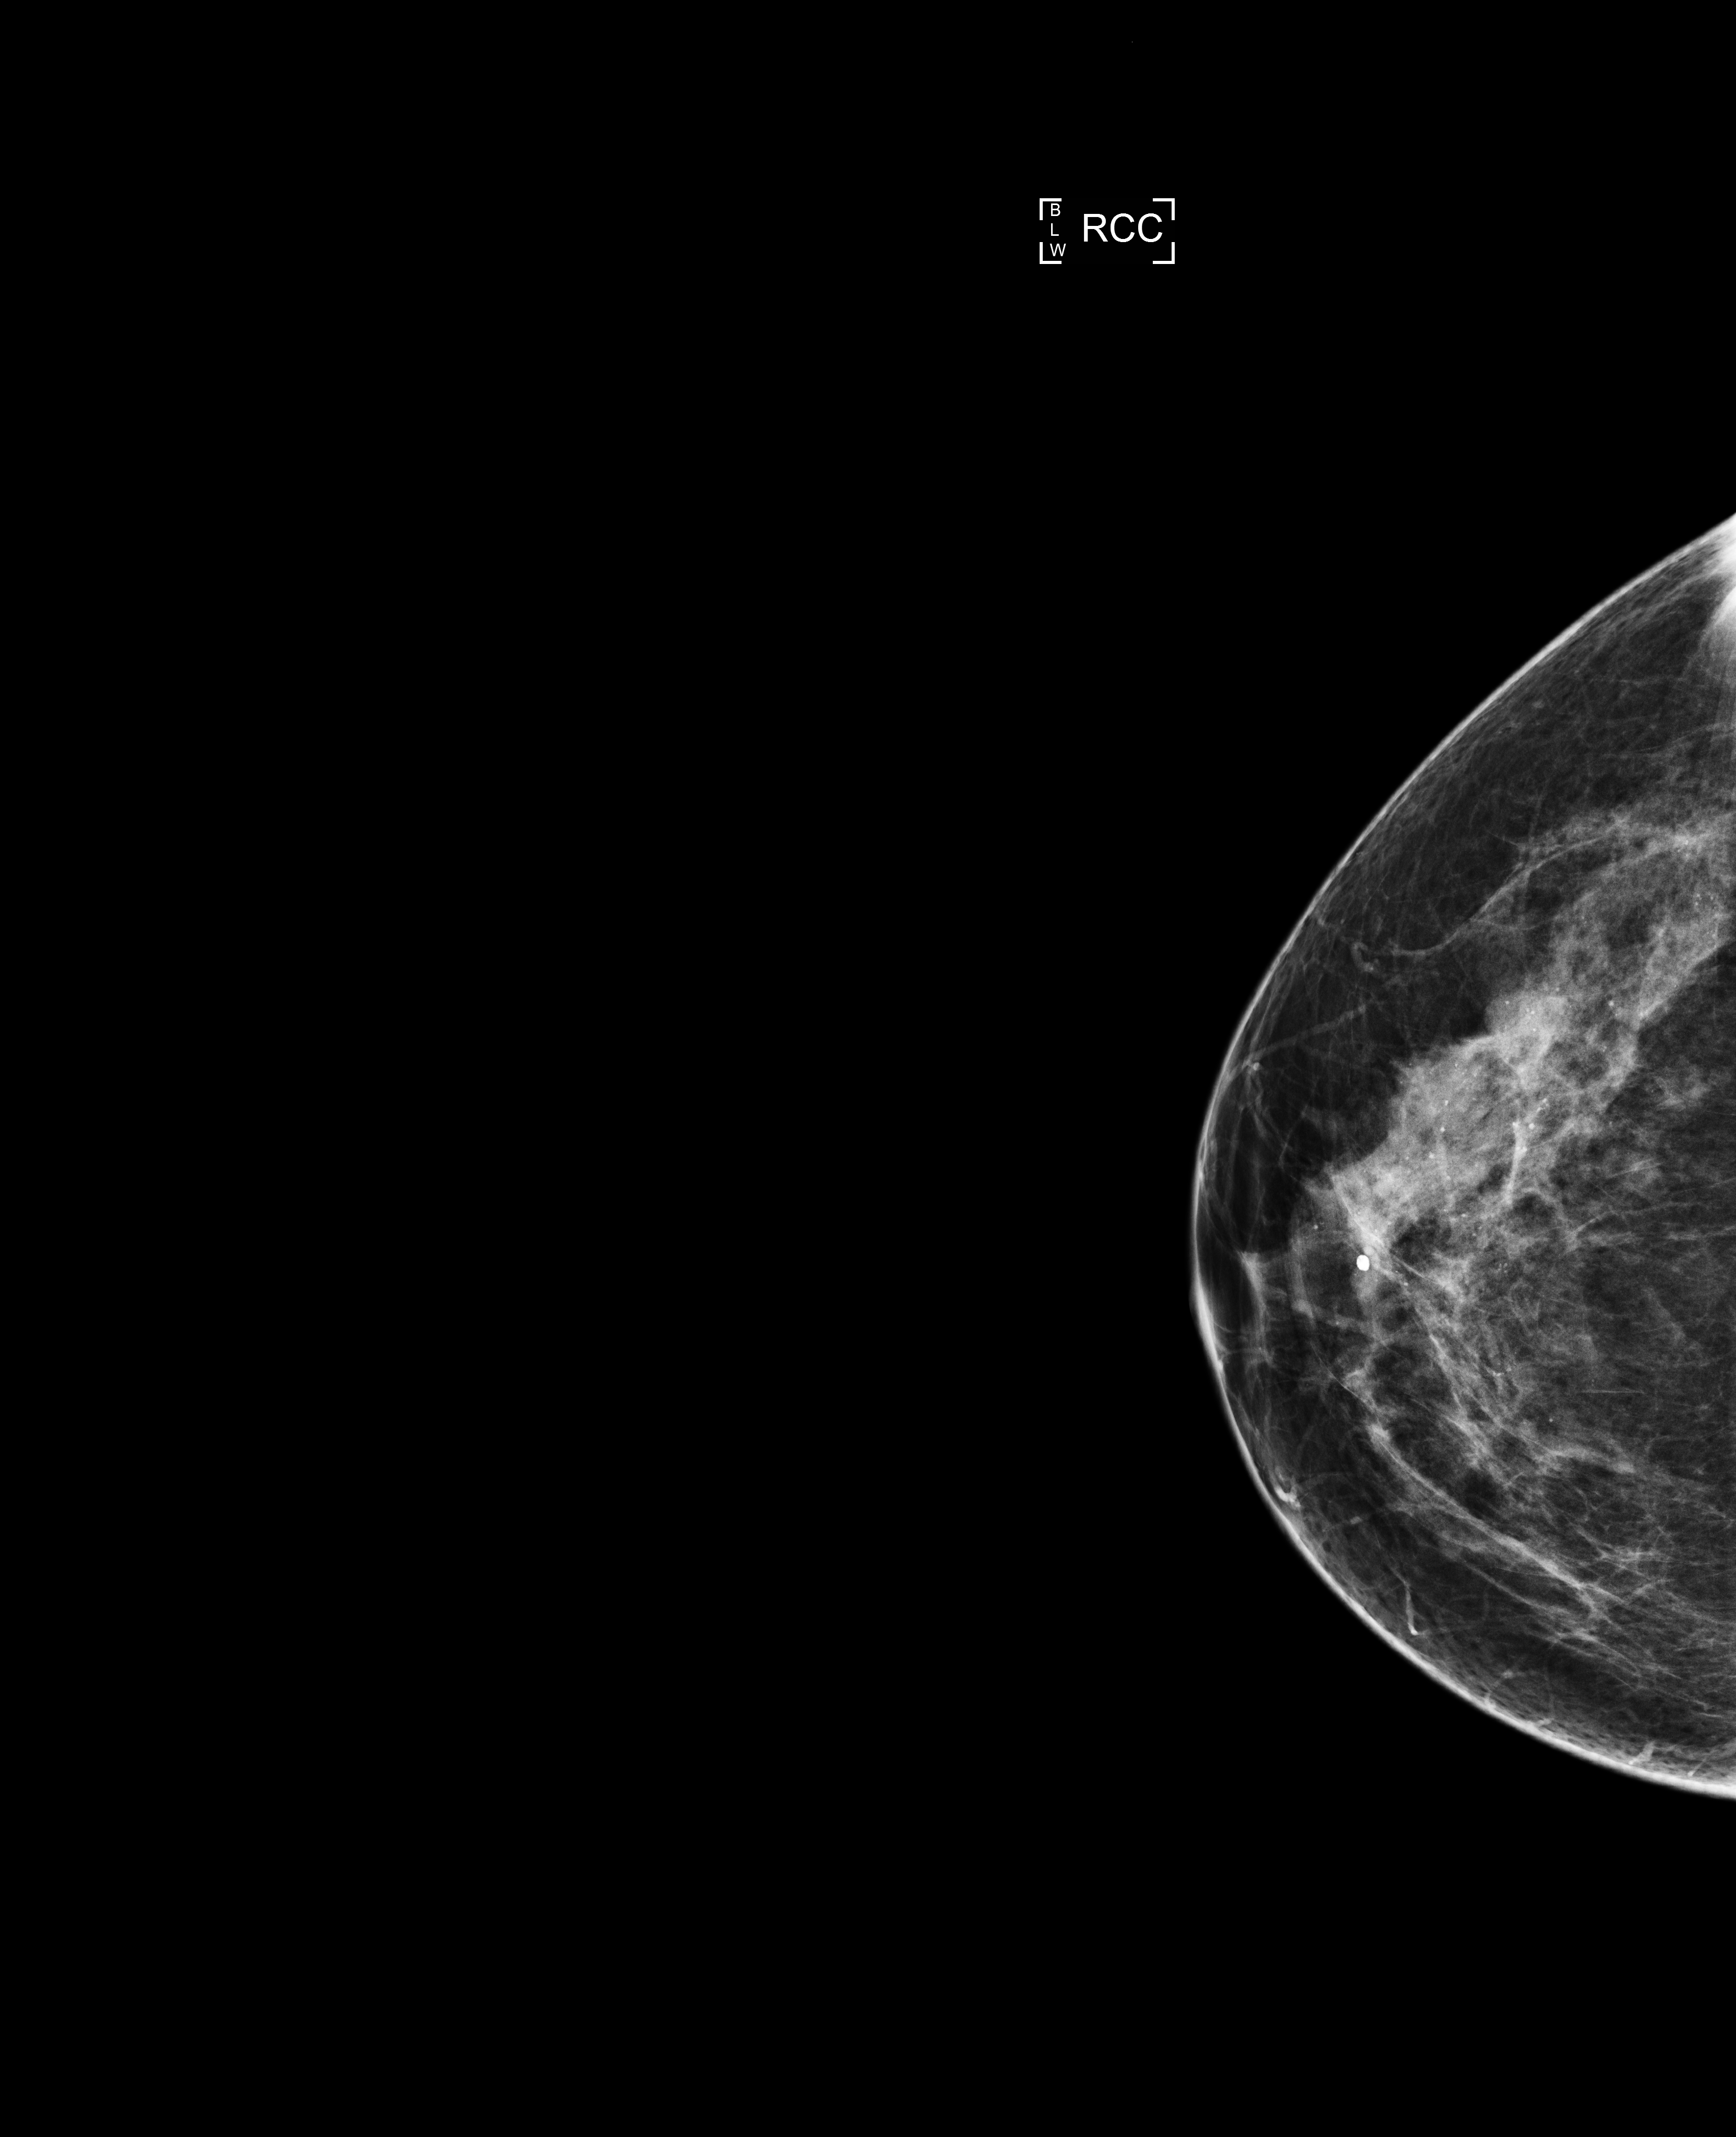
Full-field digital mammogram (FFDM), right breast, cranio-caudal projection, screening examination, system: Selenia Dimensions. Female patient, age 50 years.
BI-RADS breast density category at the screening exam (both breasts, scale 1–4): 3. Final BI-RADS assessment for this screening round (tomosynthesis exam, both breasts): category 2. Recall: no recall after this screen.